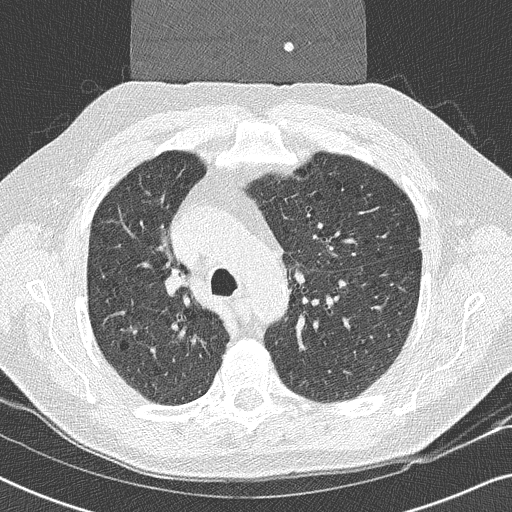
Low-dose screening chest CT, one axial slice. Slice 171 of 252 in the series (ordered by position). Reconstruction kernel B50f. Lung window (W 1500 / L -600 HU). 2 mm slice thickness. 512 × 512 image matrix, field of view 330 × 330 mm.
Annotated regions visible in this slice (expert manual segmentation):
- lesion 1 (tumor, upper lobe of right lung): box from (x=163, y=274) to (x=184, y=295) px